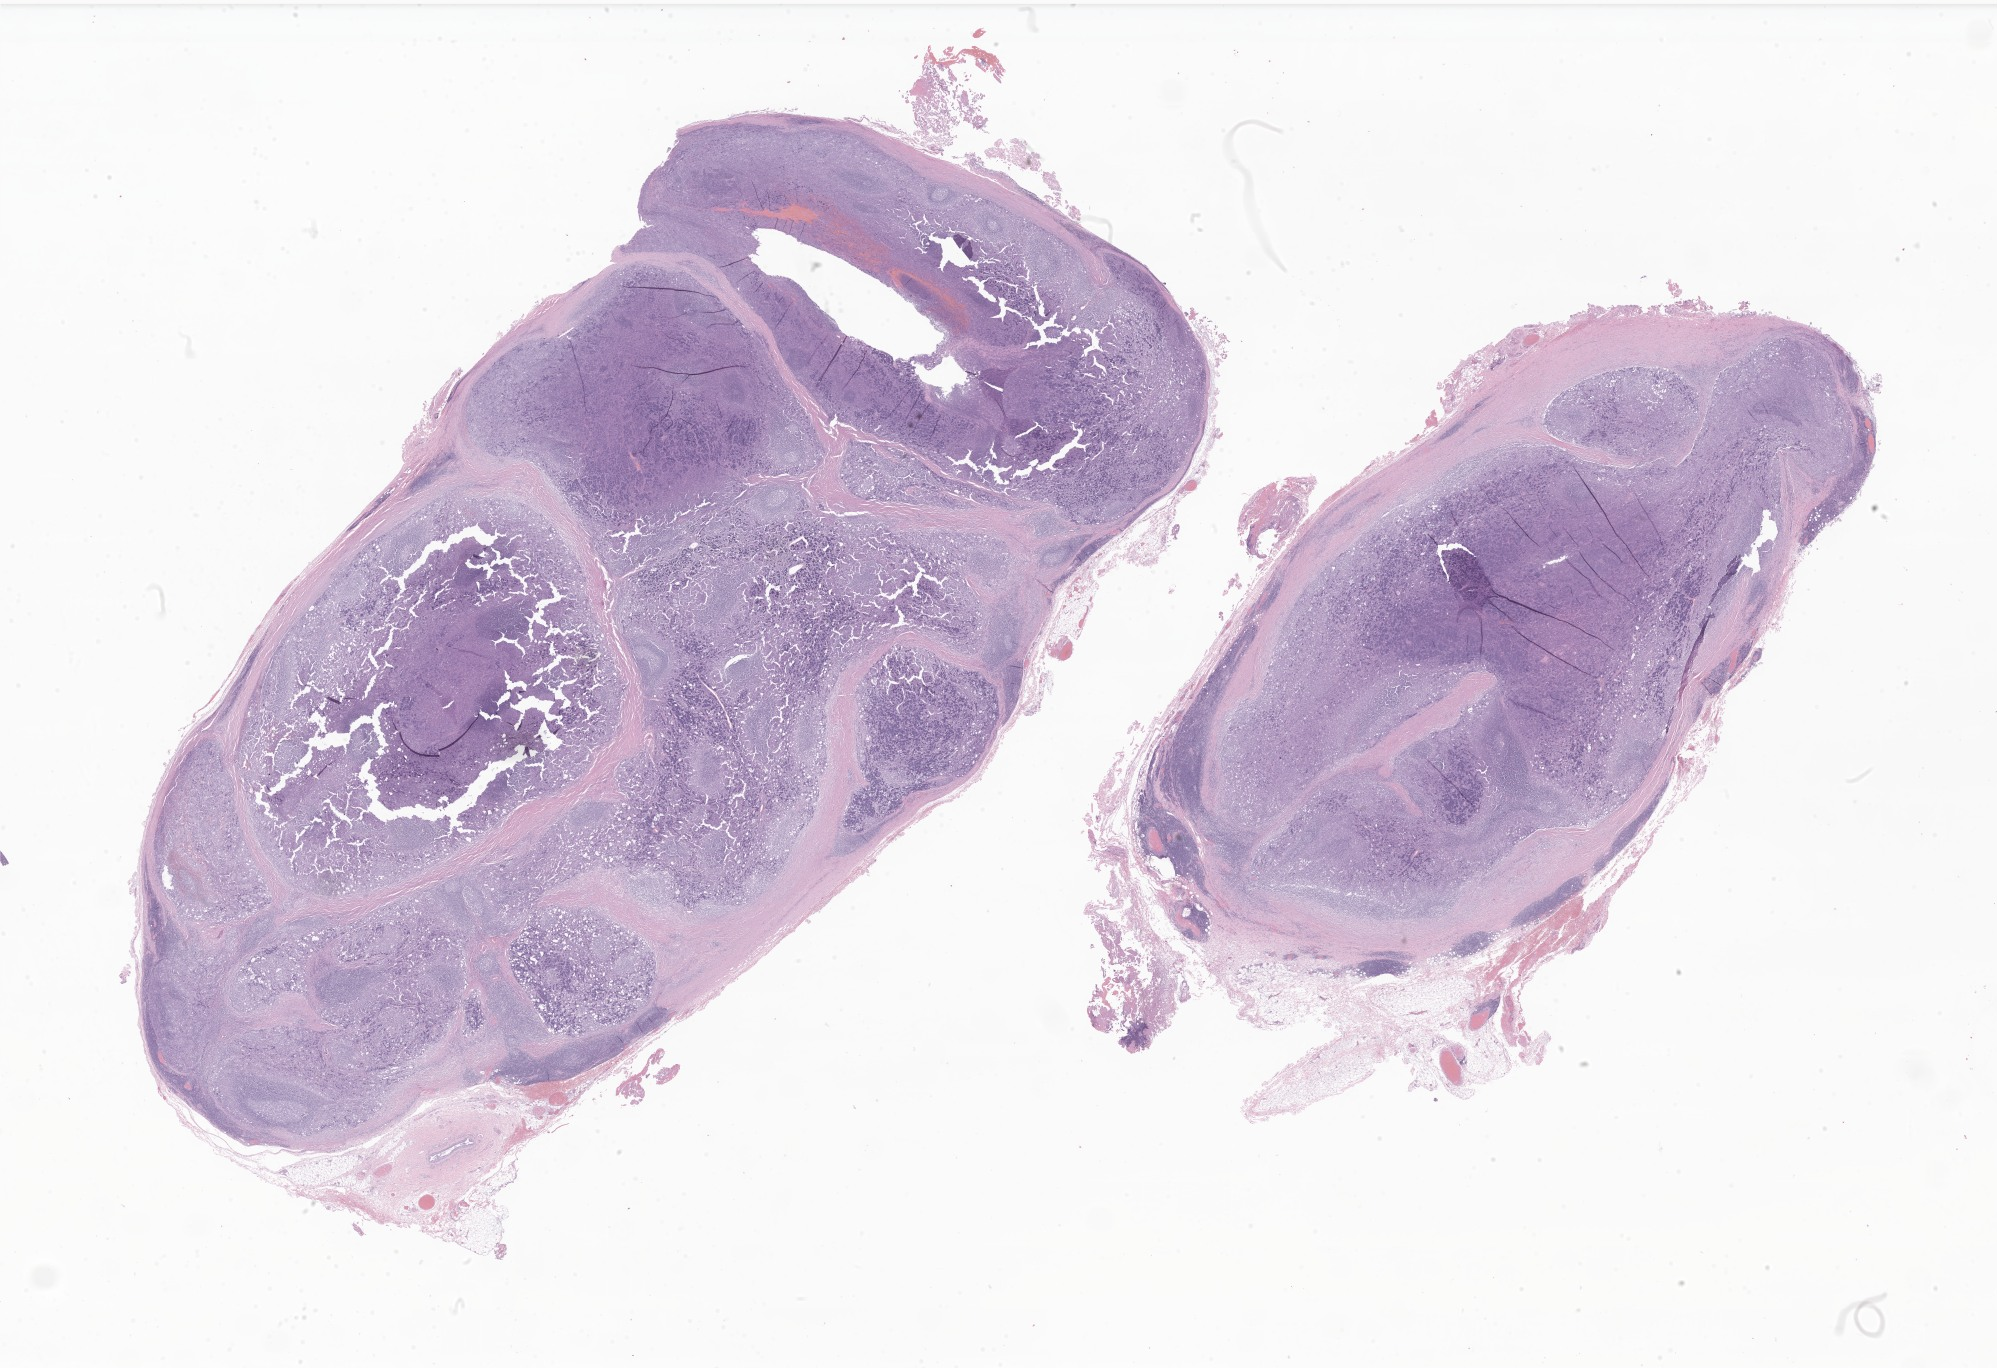
H&E whole-slide image of tumor tissue from the parotid gland, a low-resolution overview of the entire scanned area, about 33.7 x 23.1 mm, formalin-fixed paraffin-embedded section. Female patient, age 204 months (17 years).
Diagnosis: Acinar cell carcinoma.